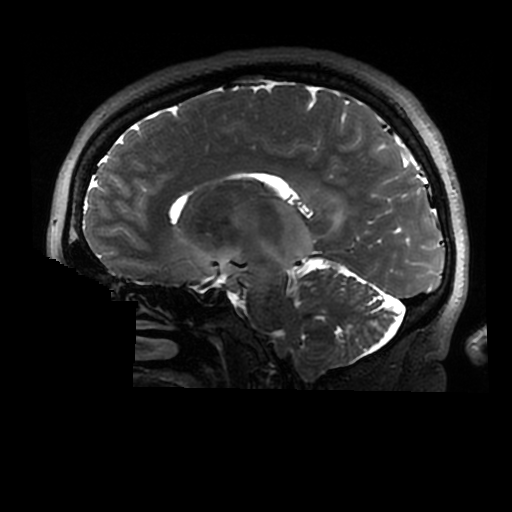
Brain MRI from a brain-tumour surgery series, one sagittal slice. Position 171 of 320 along the scan axis. 512 × 512 image matrix, field of view 240 × 240 mm. From the clinical record (not read from this slice): histopathology: Astrocytoma; WHO grade: 2; IDH mutation: yes.
Structures marked on this image (expert manual segmentation):
- tumour: bounding box (x1, y1, x2, y2) in pixels: (202, 201, 315, 292)